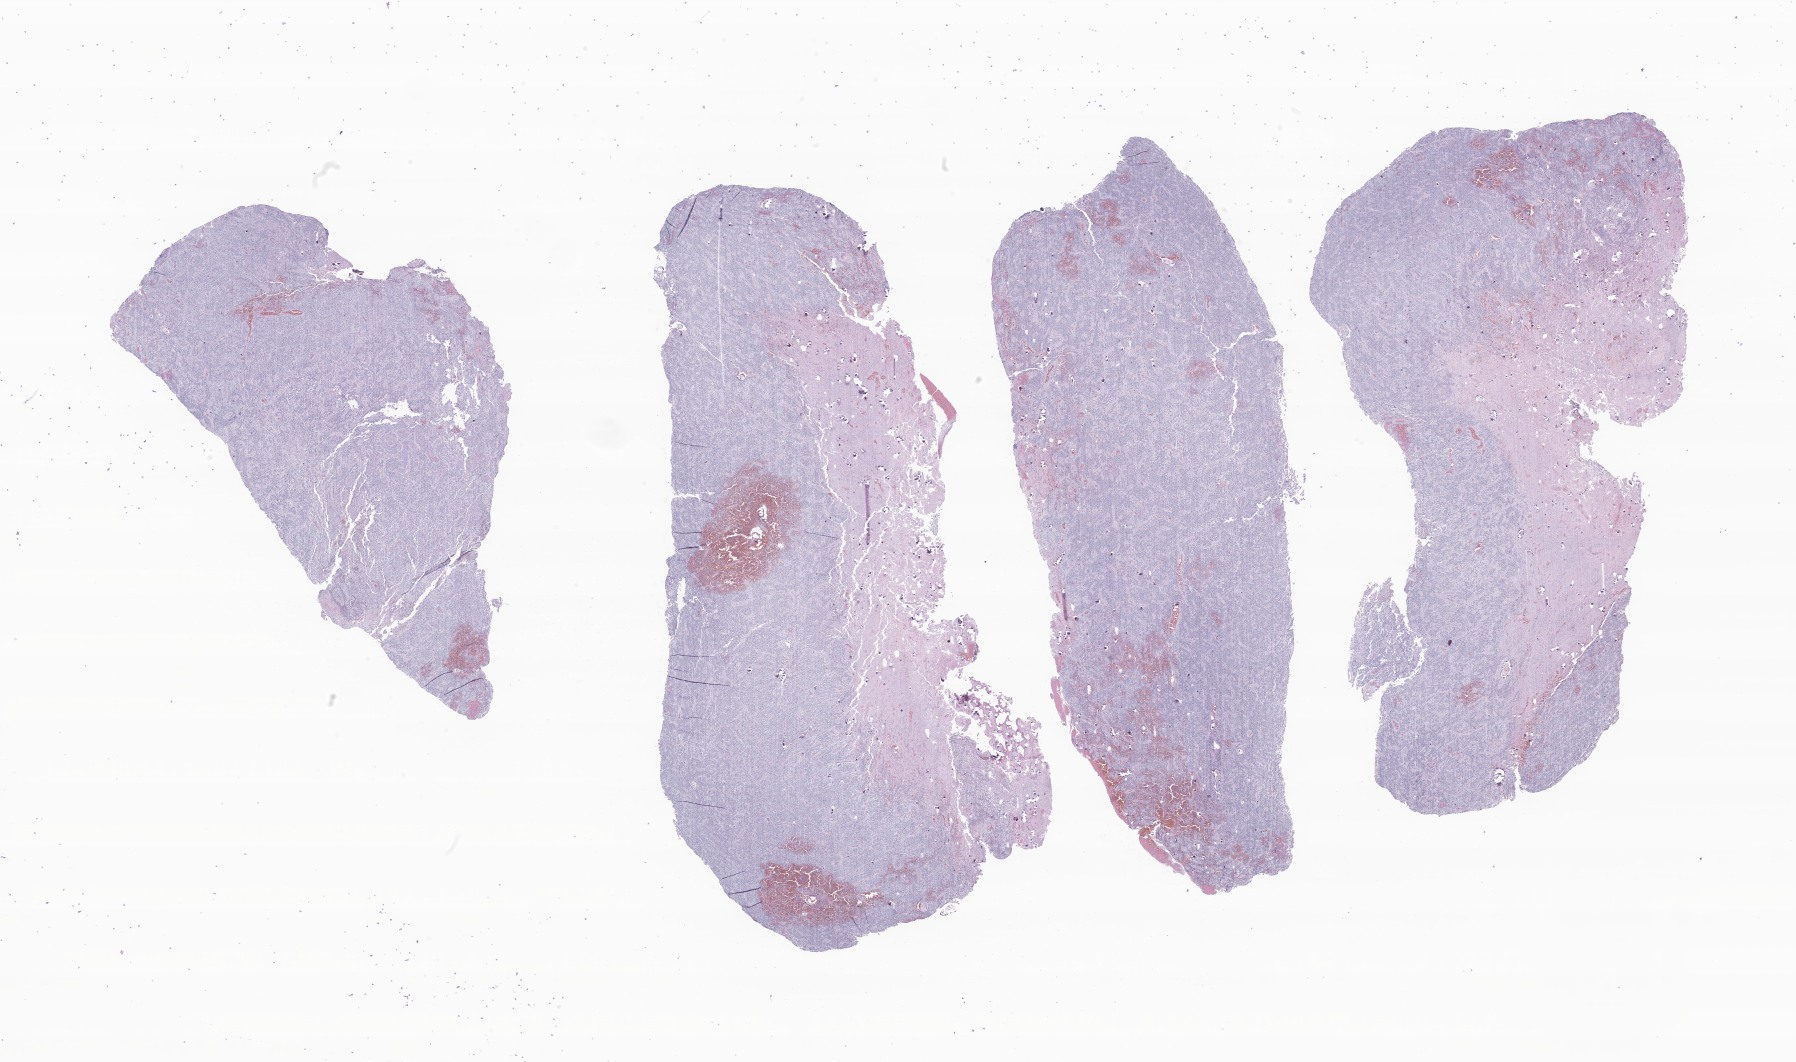
Digitized hematoxylin and eosin (H&E)-stained section of tumor tissue from the brain — a low-resolution overview of the entire scanned area, about 30.3 x 17.9 mm, FFPE section. Patient female; age 67 months (5 years 7 months).
Diagnosis: Glioma, malignant.